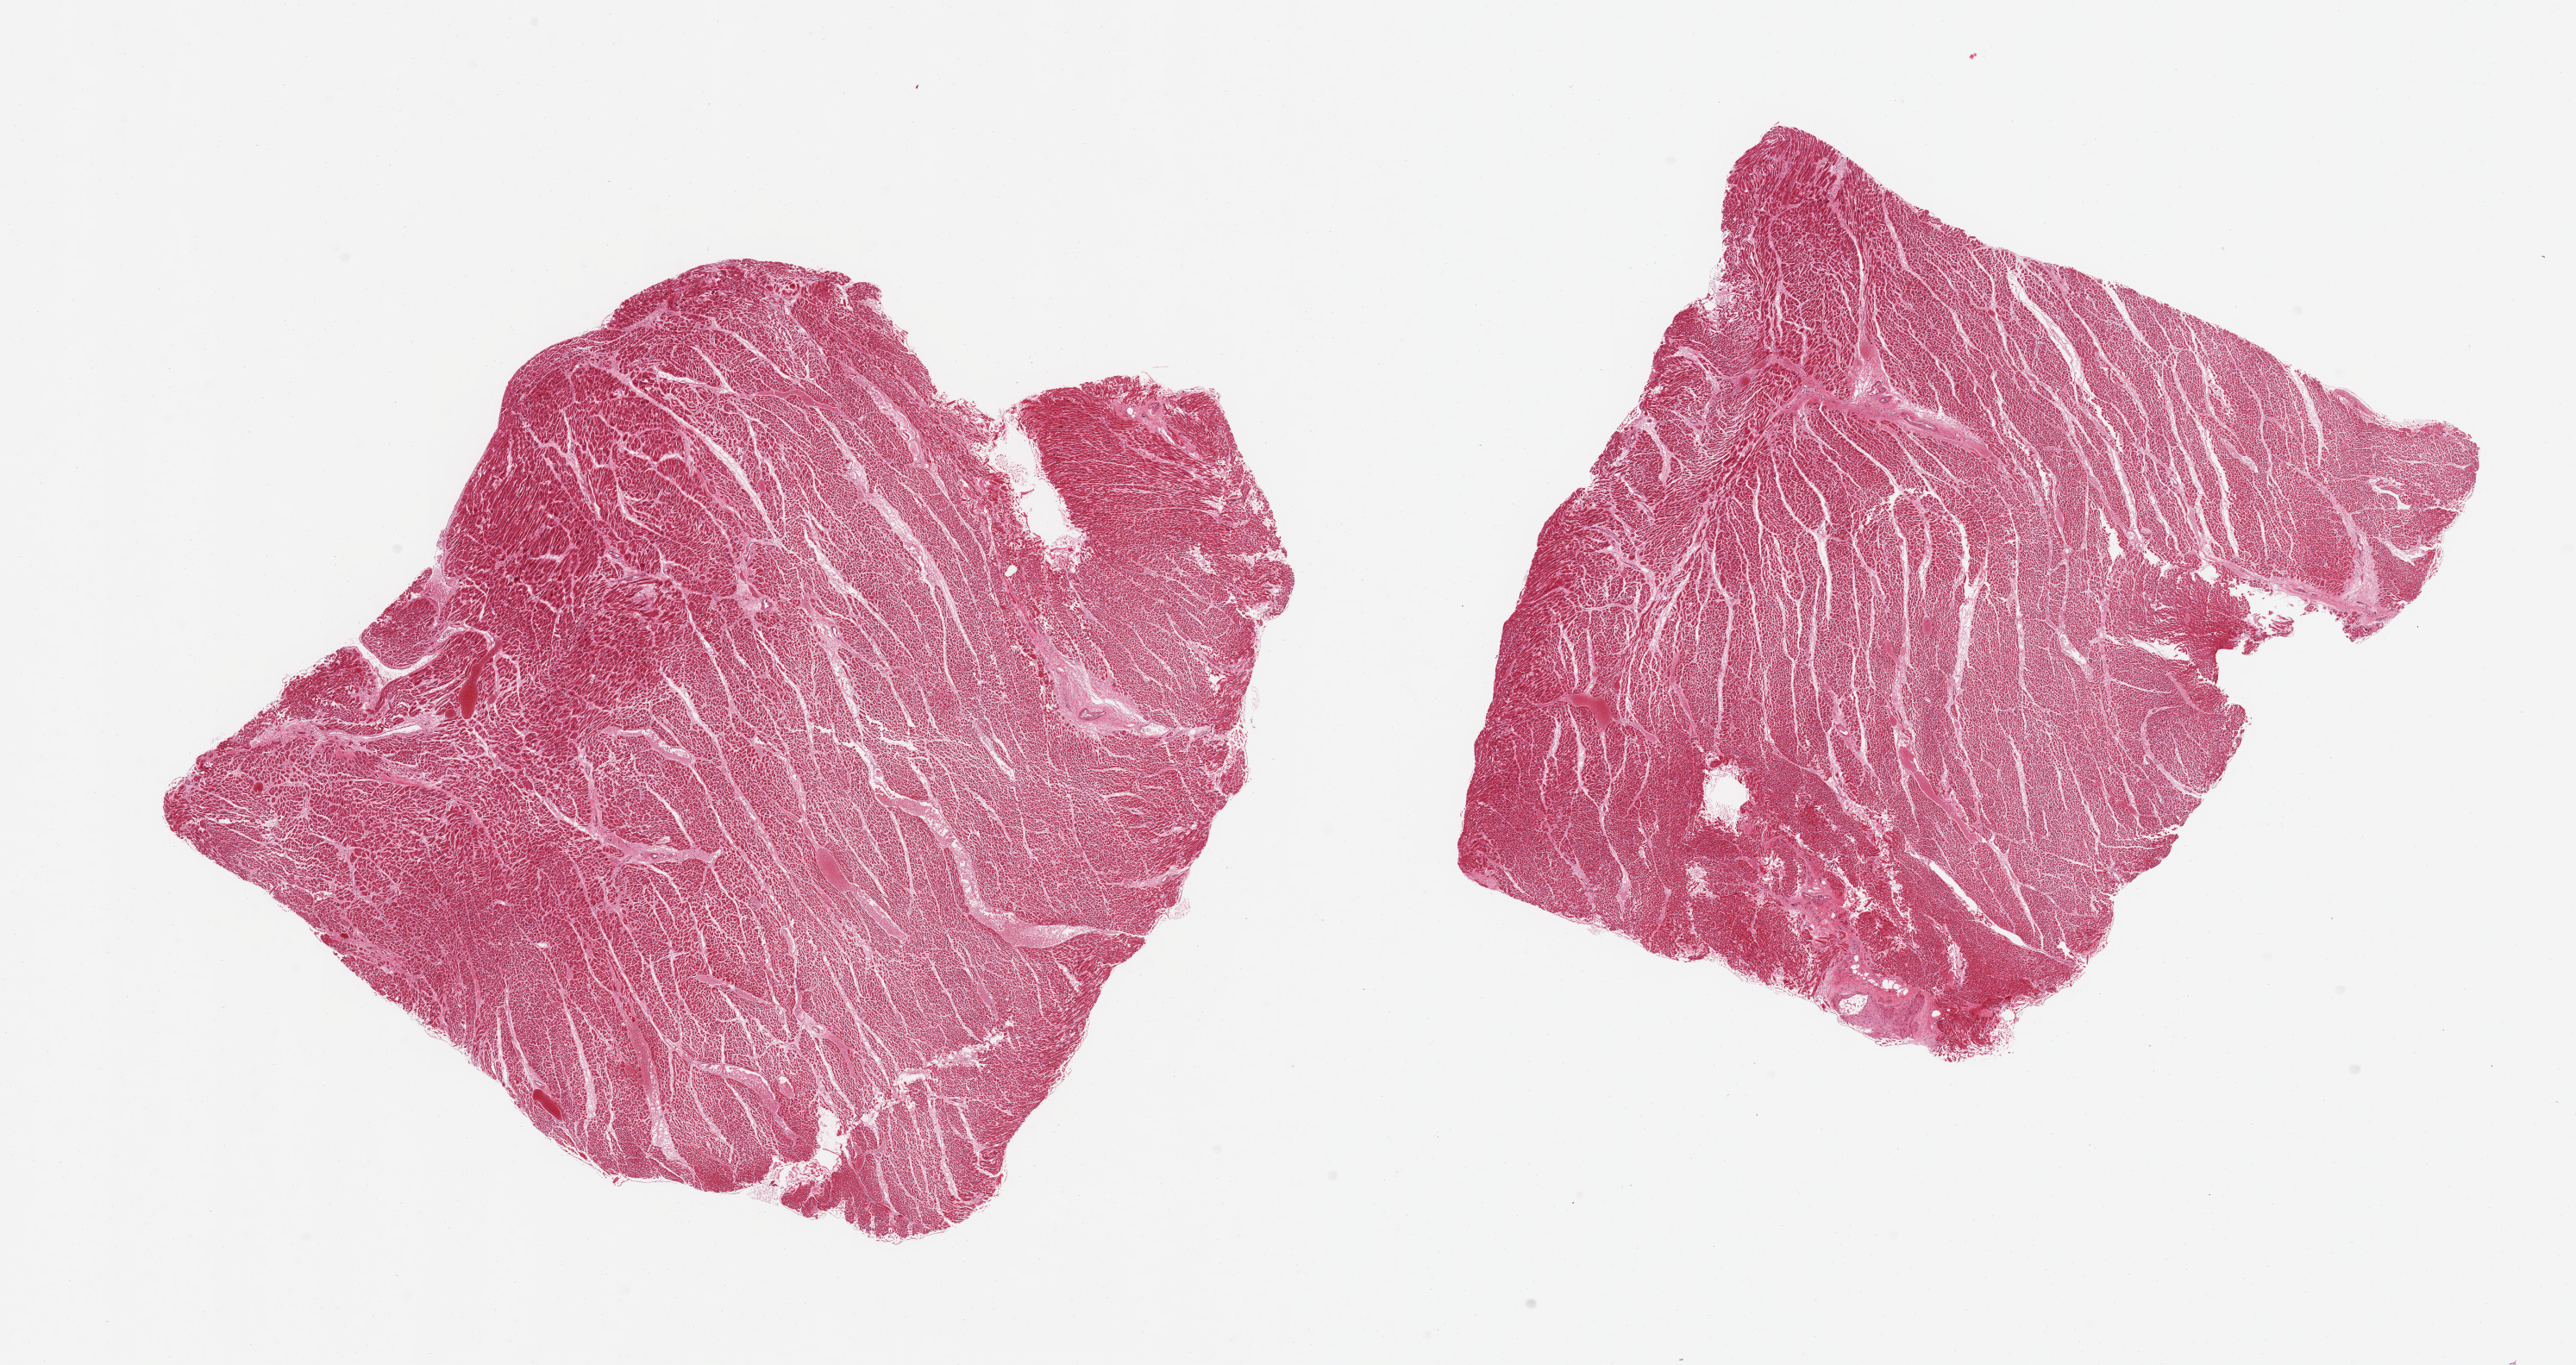
Haematoxylin and eosin whole-slide image, brightfield — a low-resolution overview of the entire scanned area, about 23.6 x 12.5 mm, PAXgene-fixed, paraffin-embedded tissue, sampled site (target tissue): heart, tissue donor sample. Donor: male.
Reviewer comment on this tissue sample: 2 pieces; some patchy increased eosinophilia (?recent ischemia).